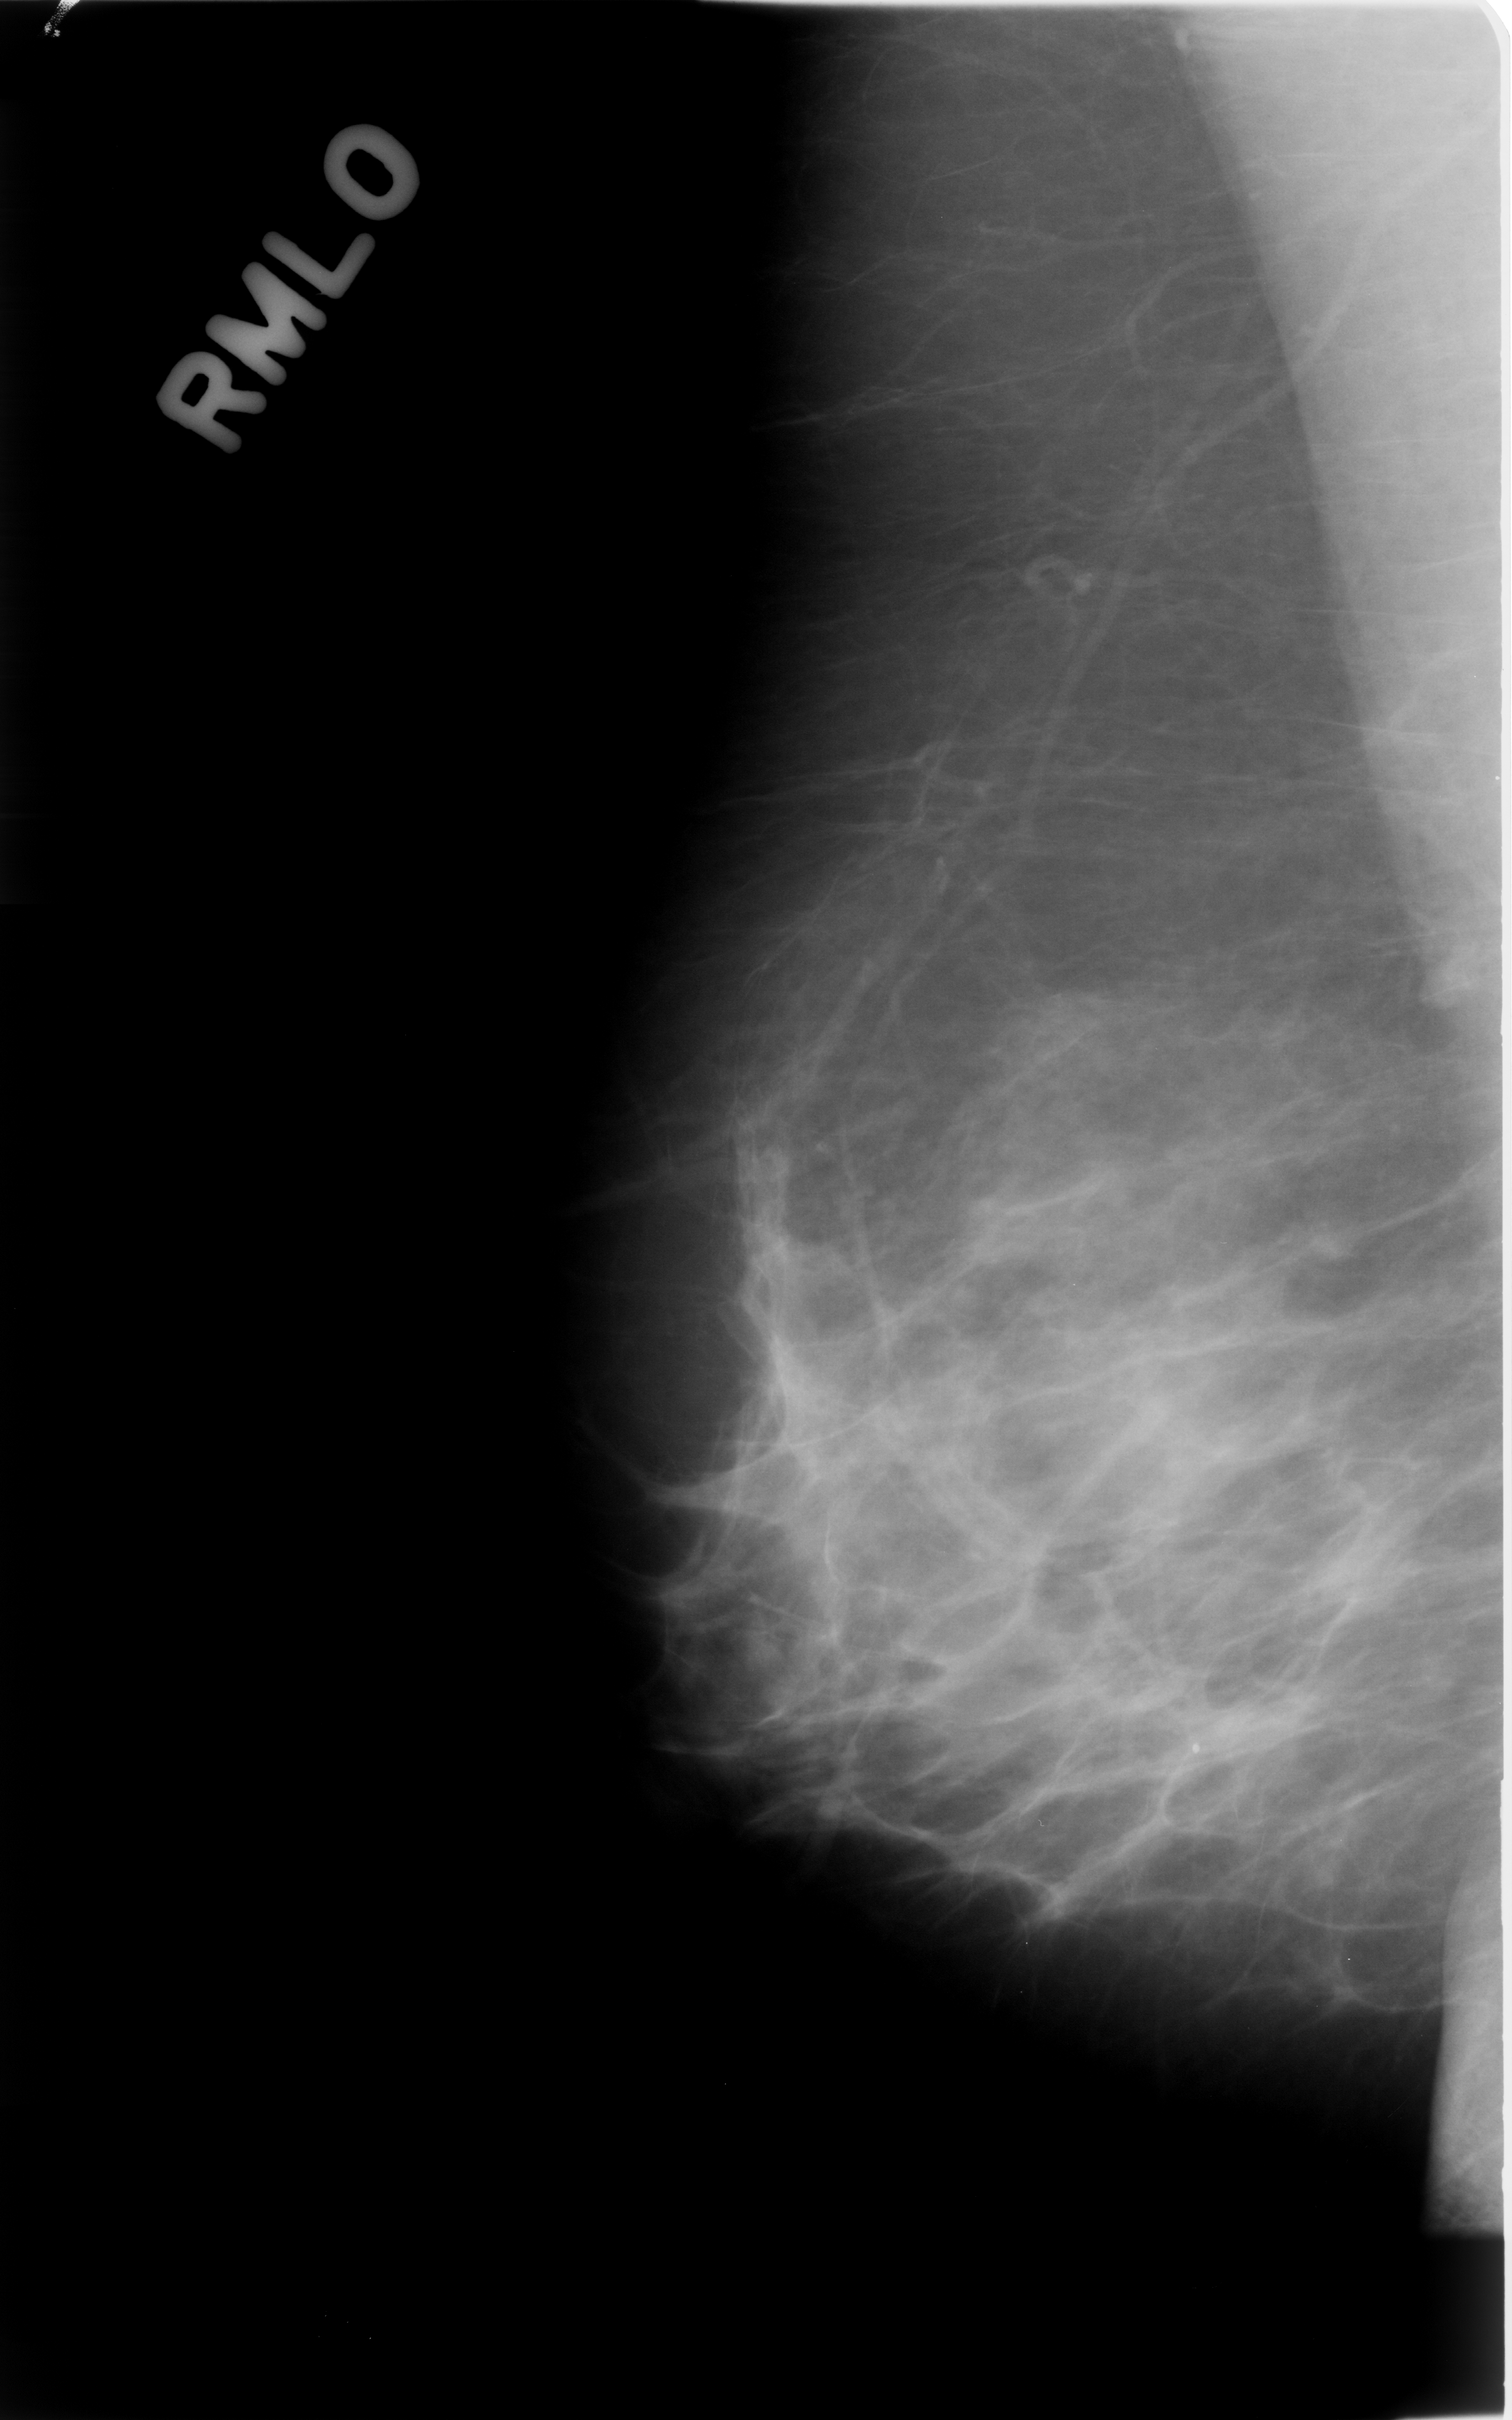
Scanned film-screen mammogram; right breast; mediolateral oblique (MLO) view; breast composition: scattered fibroglandular densities (BI-RADS density category 2 of 4); 1512 × 2420 image matrix.
Marked abnormalities (boxes around the expert regions of interest):
- mass, shape lobulated, margins microlobulated; BI-RADS assessment category 3; outcome (as recorded, no biopsy): benign without callback (not worked up further): bounding box (x1, y1, x2, y2) in pixels: (1416, 940, 1487, 1013)